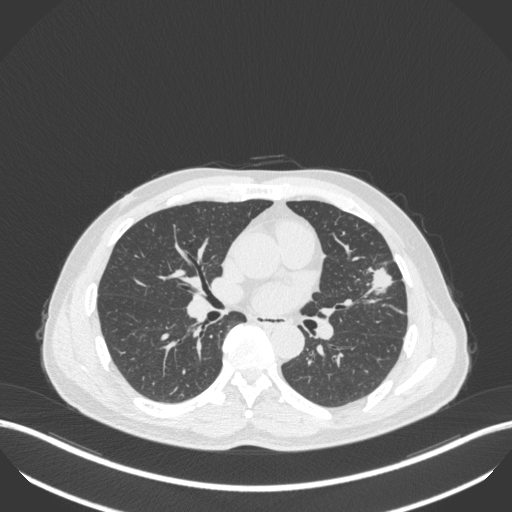
Chest CT, one axial slice; slice 208 of 418 in the series (ordered by position); reconstruction kernel B31f; 120 kVp; lung window (W 1500 / L -600 HU); 512 × 512 image matrix, field of view 400 × 400 mm. Patient: male, 55 years. From the clinical record (not read from this slice): clinical TNM (as recorded): T1c N0 M0; histopathological grade: G2-3.
Outlined on this slice (bounding box drawn by a radiologist):
- lung tumour (recorded histology: adenocarcinoma): box from (x=365, y=265) to (x=401, y=297) px